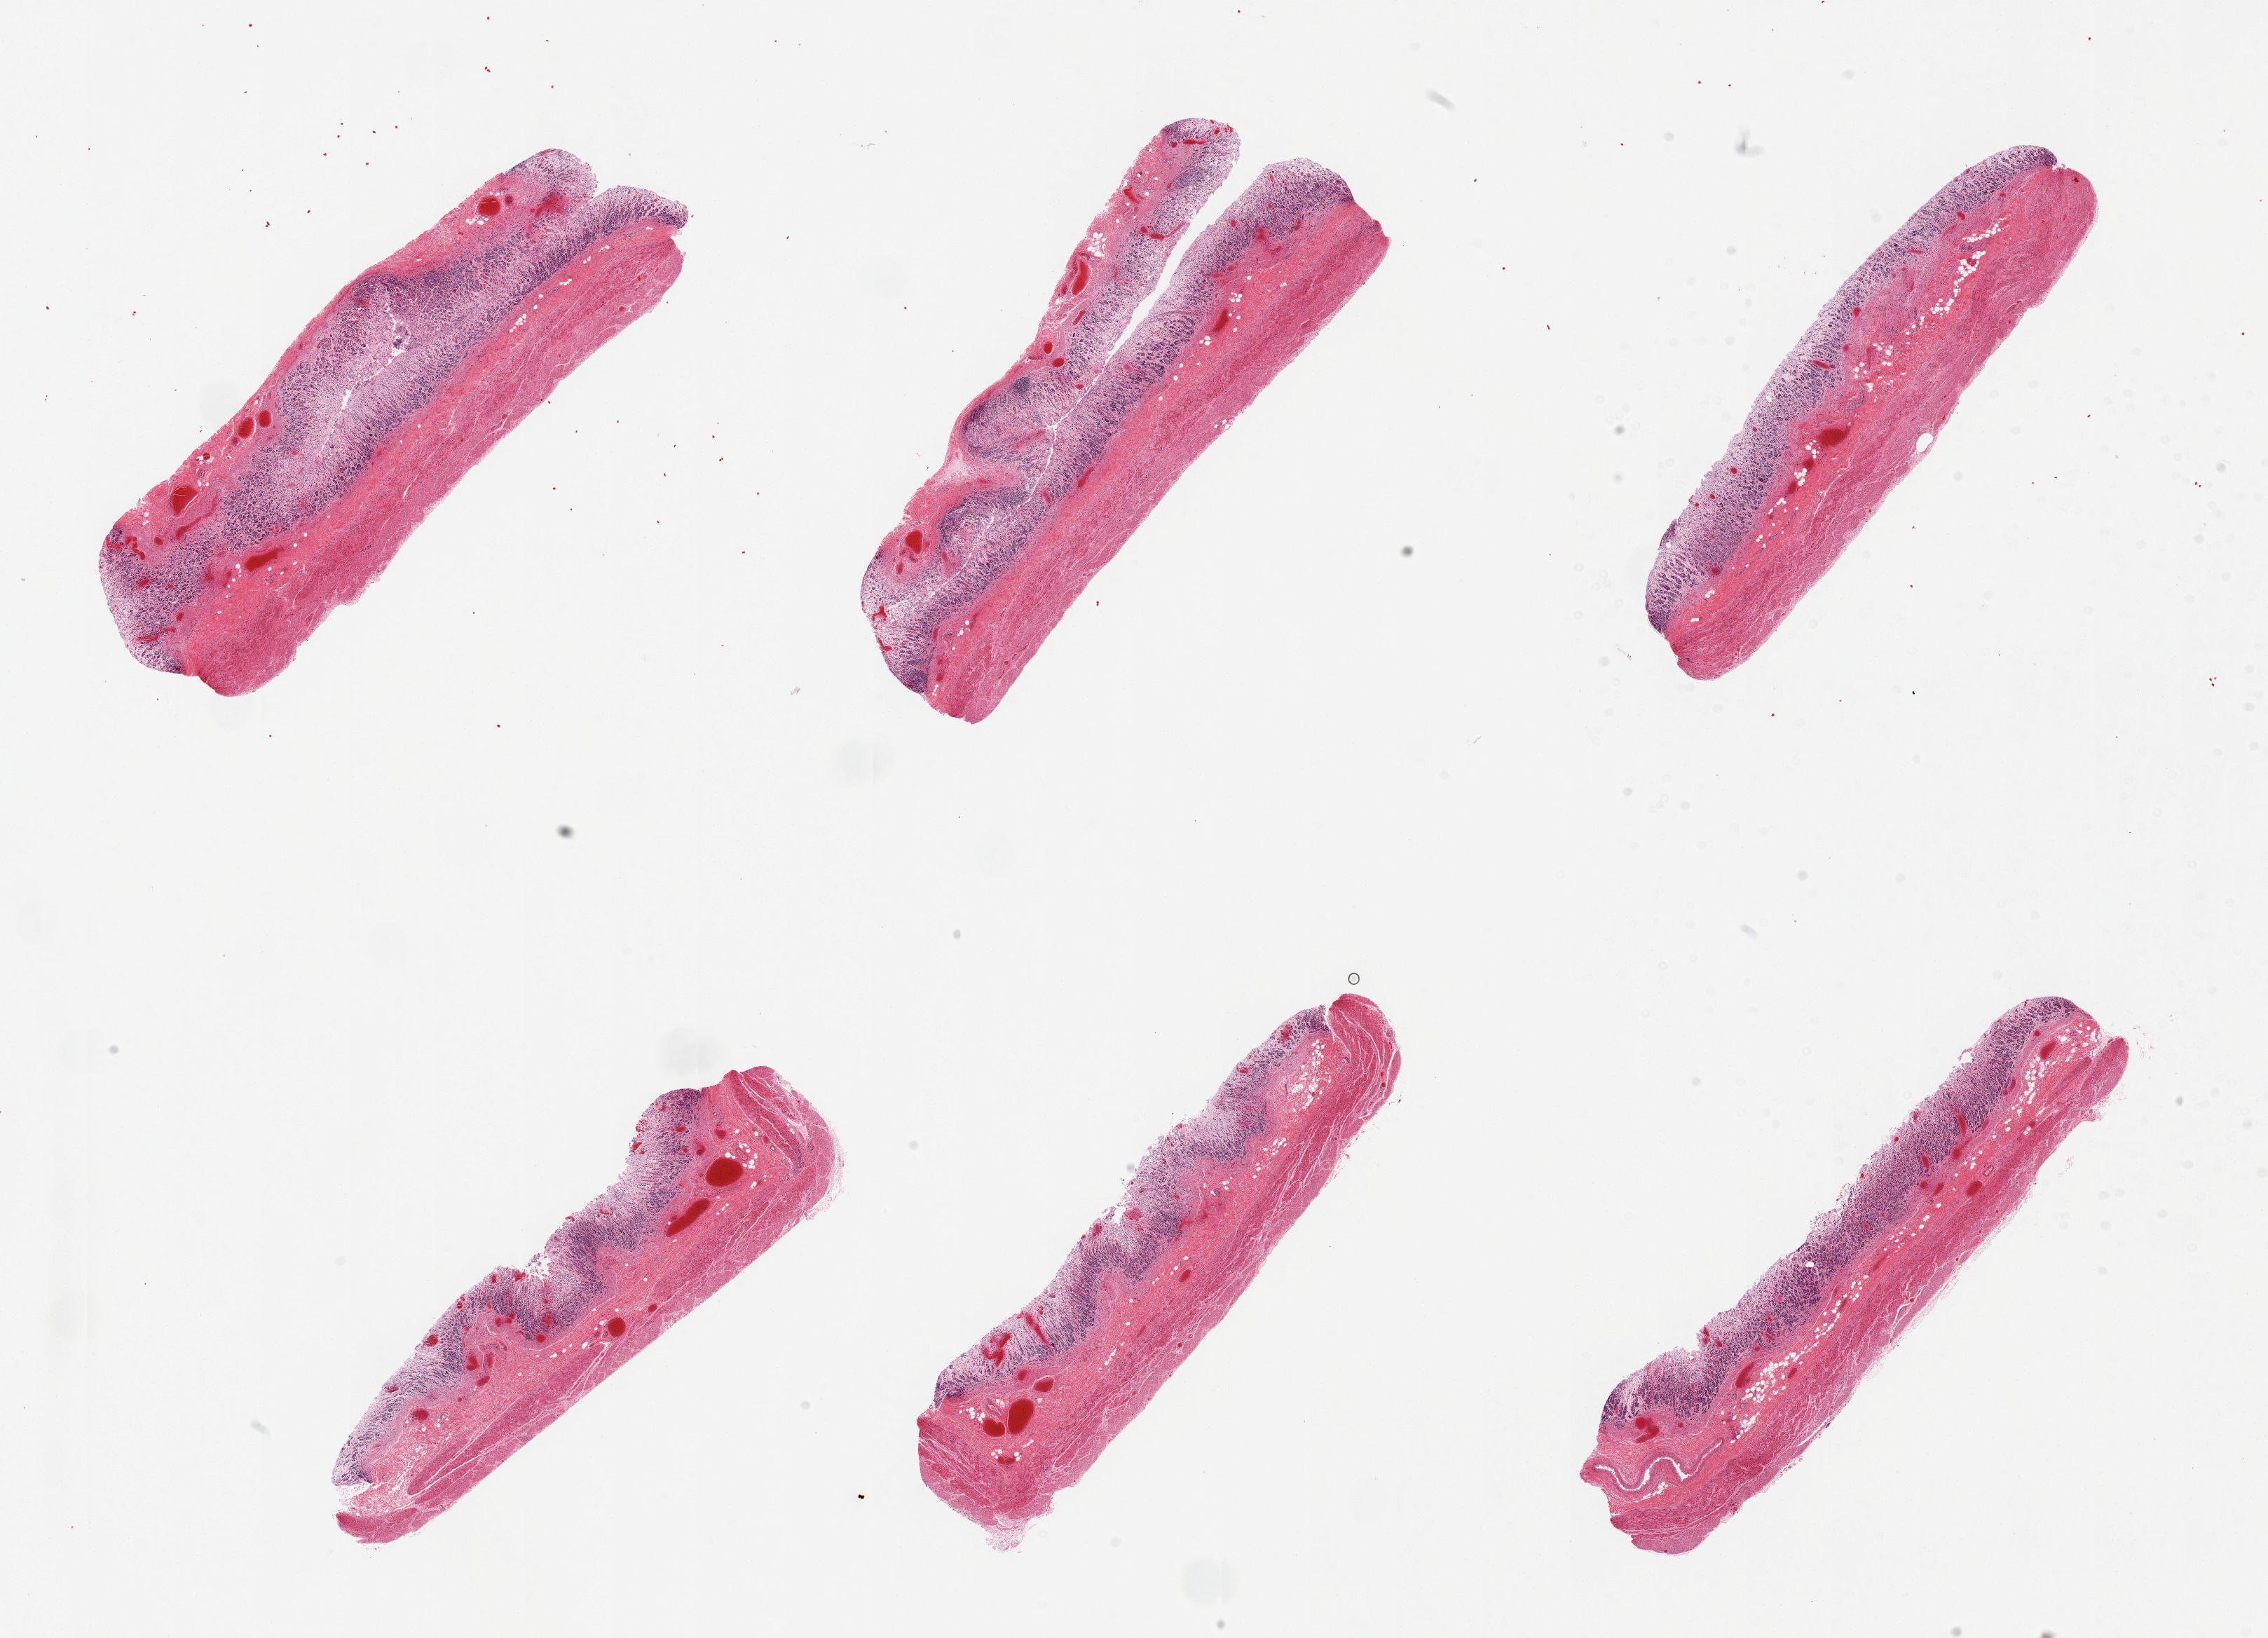
Digitized haematoxylin and eosin-stained section — whole scanned area (about 25.6 x 18.5 mm) shown as a low-resolution overview. Donor: female.
Specimen: PAXgene-fixed, paraffin-embedded tissue; section of stomach (target tissue); donor tissue sample.